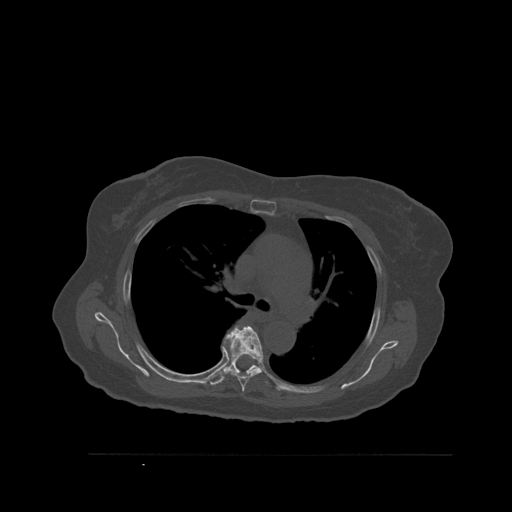
CT including the spine, one axial slice; slice 389 of 527 in the series (ordered by position); bone window (W 1800 / L 400 HU); 1.5 mm slice thickness; 512 × 512 image matrix, field of view 470 × 470 mm. Female patient, age 73 years. From the clinical record (not read from this slice): primary cancer: breast.
Outlined on this slice (semi-automatic segmentation, software-assisted and operator-edited):
- T5 vertebra: box from (x=226, y=325) to (x=263, y=392) px
- T6 vertebra: (x=207, y=325)–(x=271, y=387)